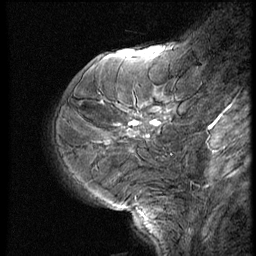
Breast MRI (dynamic contrast-enhanced), one sagittal slice. Position 17 of 52 along the scan axis. Dynamic contrast-enhanced series, image 2 of 3 at this slice position (ordered by acquisition). 1.5 T. TE 4.2 ms, TR 9 ms. 2.5 mm slice thickness. 256 × 256 image matrix. Patient: female, 62 years. From the clinical record (not read from this slice): setting: breast cancer imaged before/during neoadjuvant chemotherapy; receptor status: HR-positive, HER2-negative.
Structures marked on this image (semi-automatically segmented with operator editing):
- analysis volume of interest (the breast-tissue region the enhancement analysis was run in; not a lesion): box from (x=67, y=94) to (x=182, y=177) px
- tumour enhancement mask (voxels above the 140 % enhancement threshold inside the analysis volume of interest): (x=135, y=123)–(x=139, y=125)